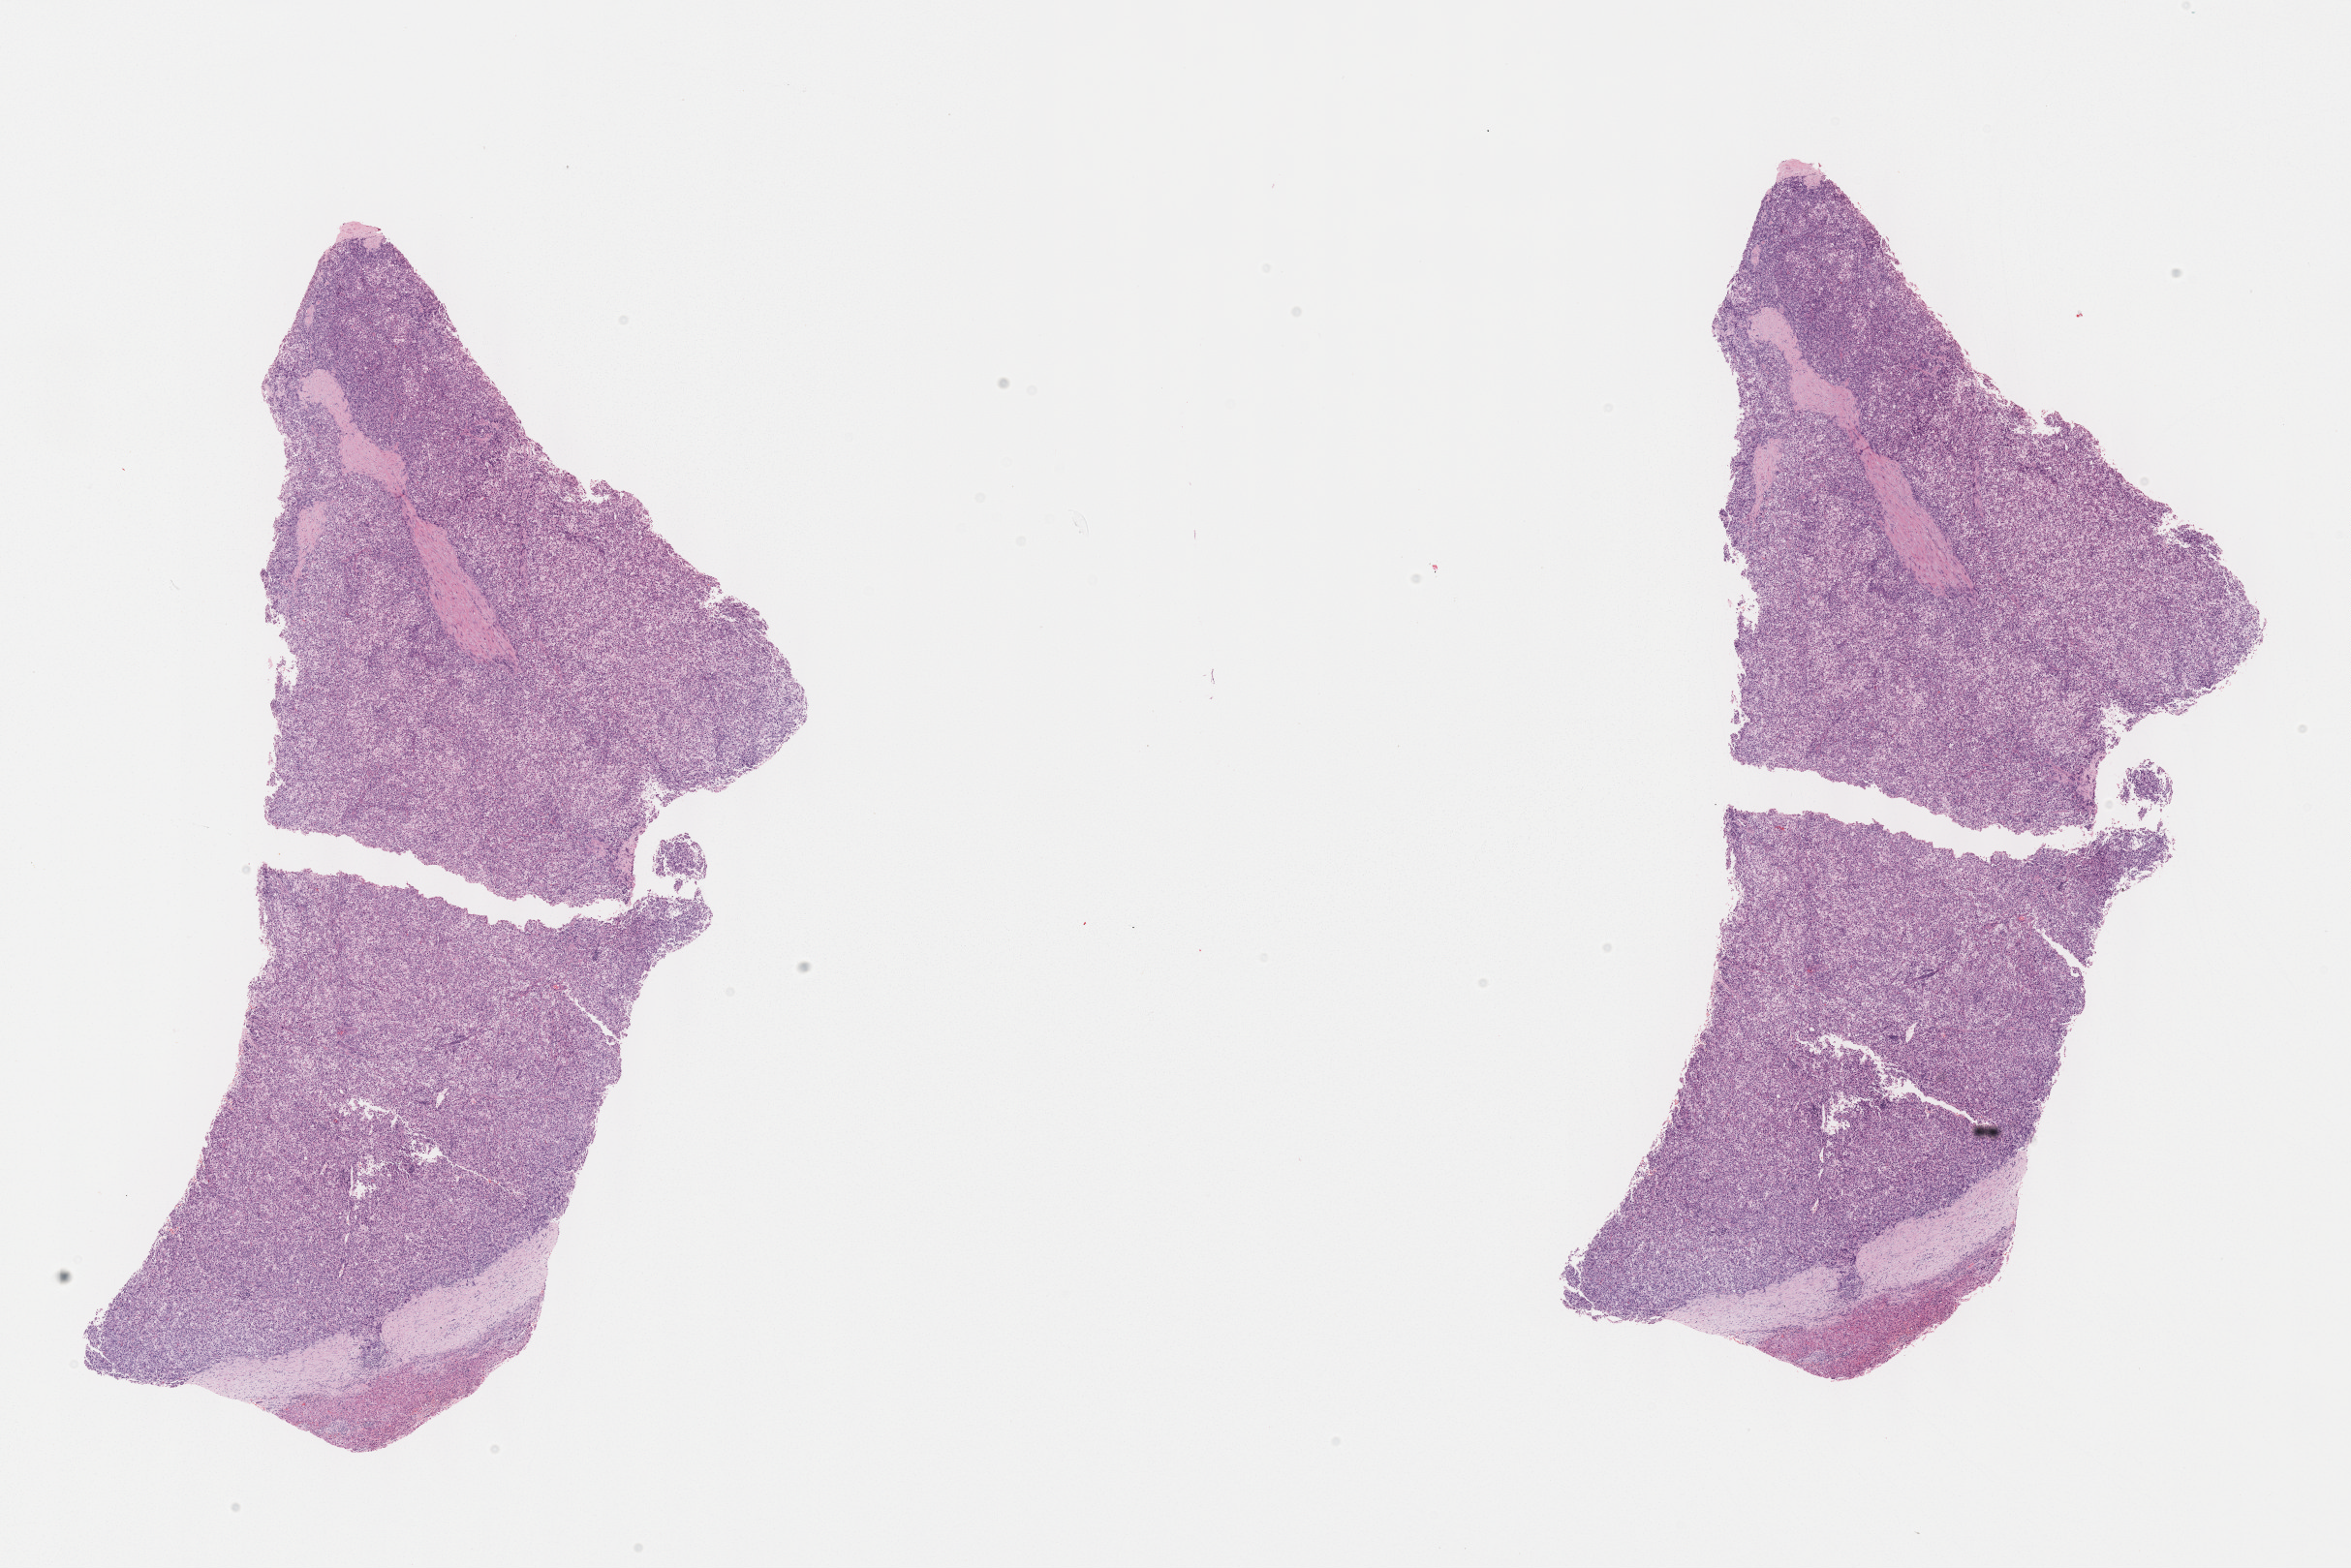
Whole-slide histology image, Hematoxylin and eosin (H&E) stained — low-resolution overview of the scanned area, about 19.6 x 13.1 mm, formalin-fixed paraffin-embedded (FFPE) diagnostic section, sample: primary tumour, liver. Patient: male, age at initial diagnosis 32 years. Histologic grade: G3 (poorly differentiated).
Histologic diagnosis: Hepatocellular carcinoma, NOS. AJCC pathologic stage: I.